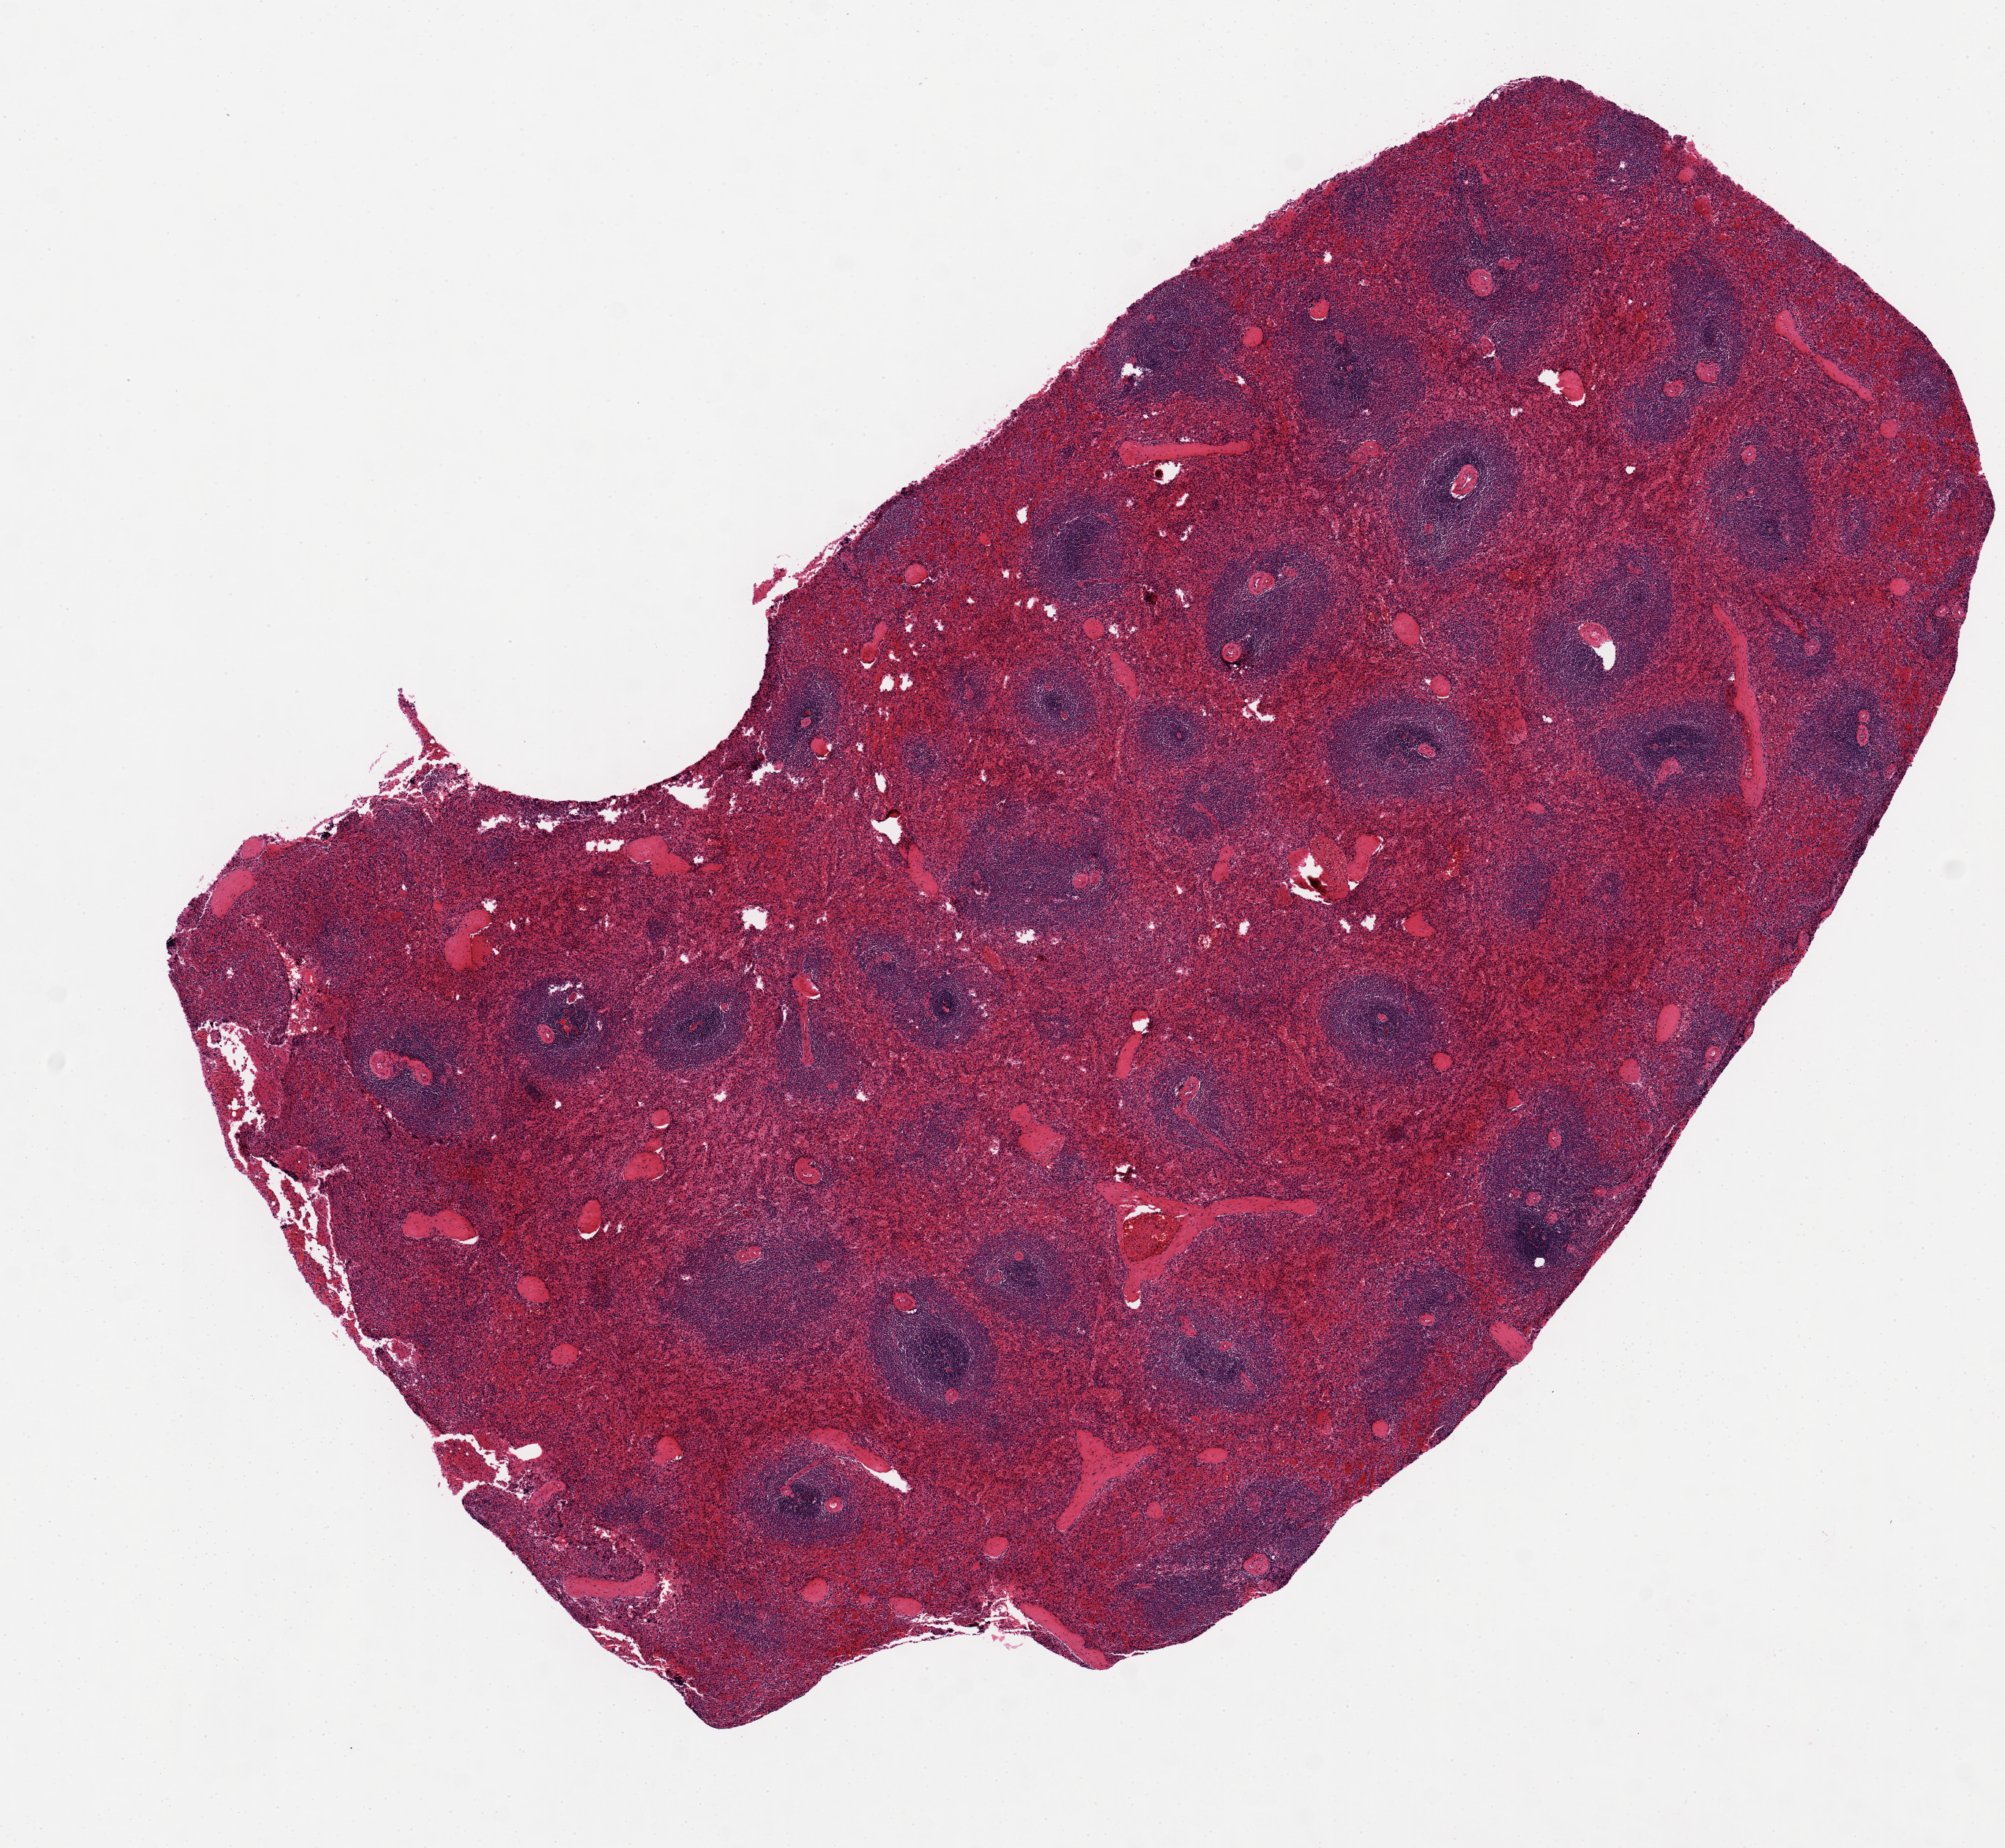
Whole-slide image, H&E stain, brightfield — whole scanned area (about 10.8 x 10.0 mm) shown as a low-resolution overview. PAXgene-fixed paraffin-embedded (PFPE) section. Sampled site (target tissue): spleen. Donor tissue sample. Donor sex: male.
• review note (as recorded): 9.7x5.5mm. Foci appear poorly fixed